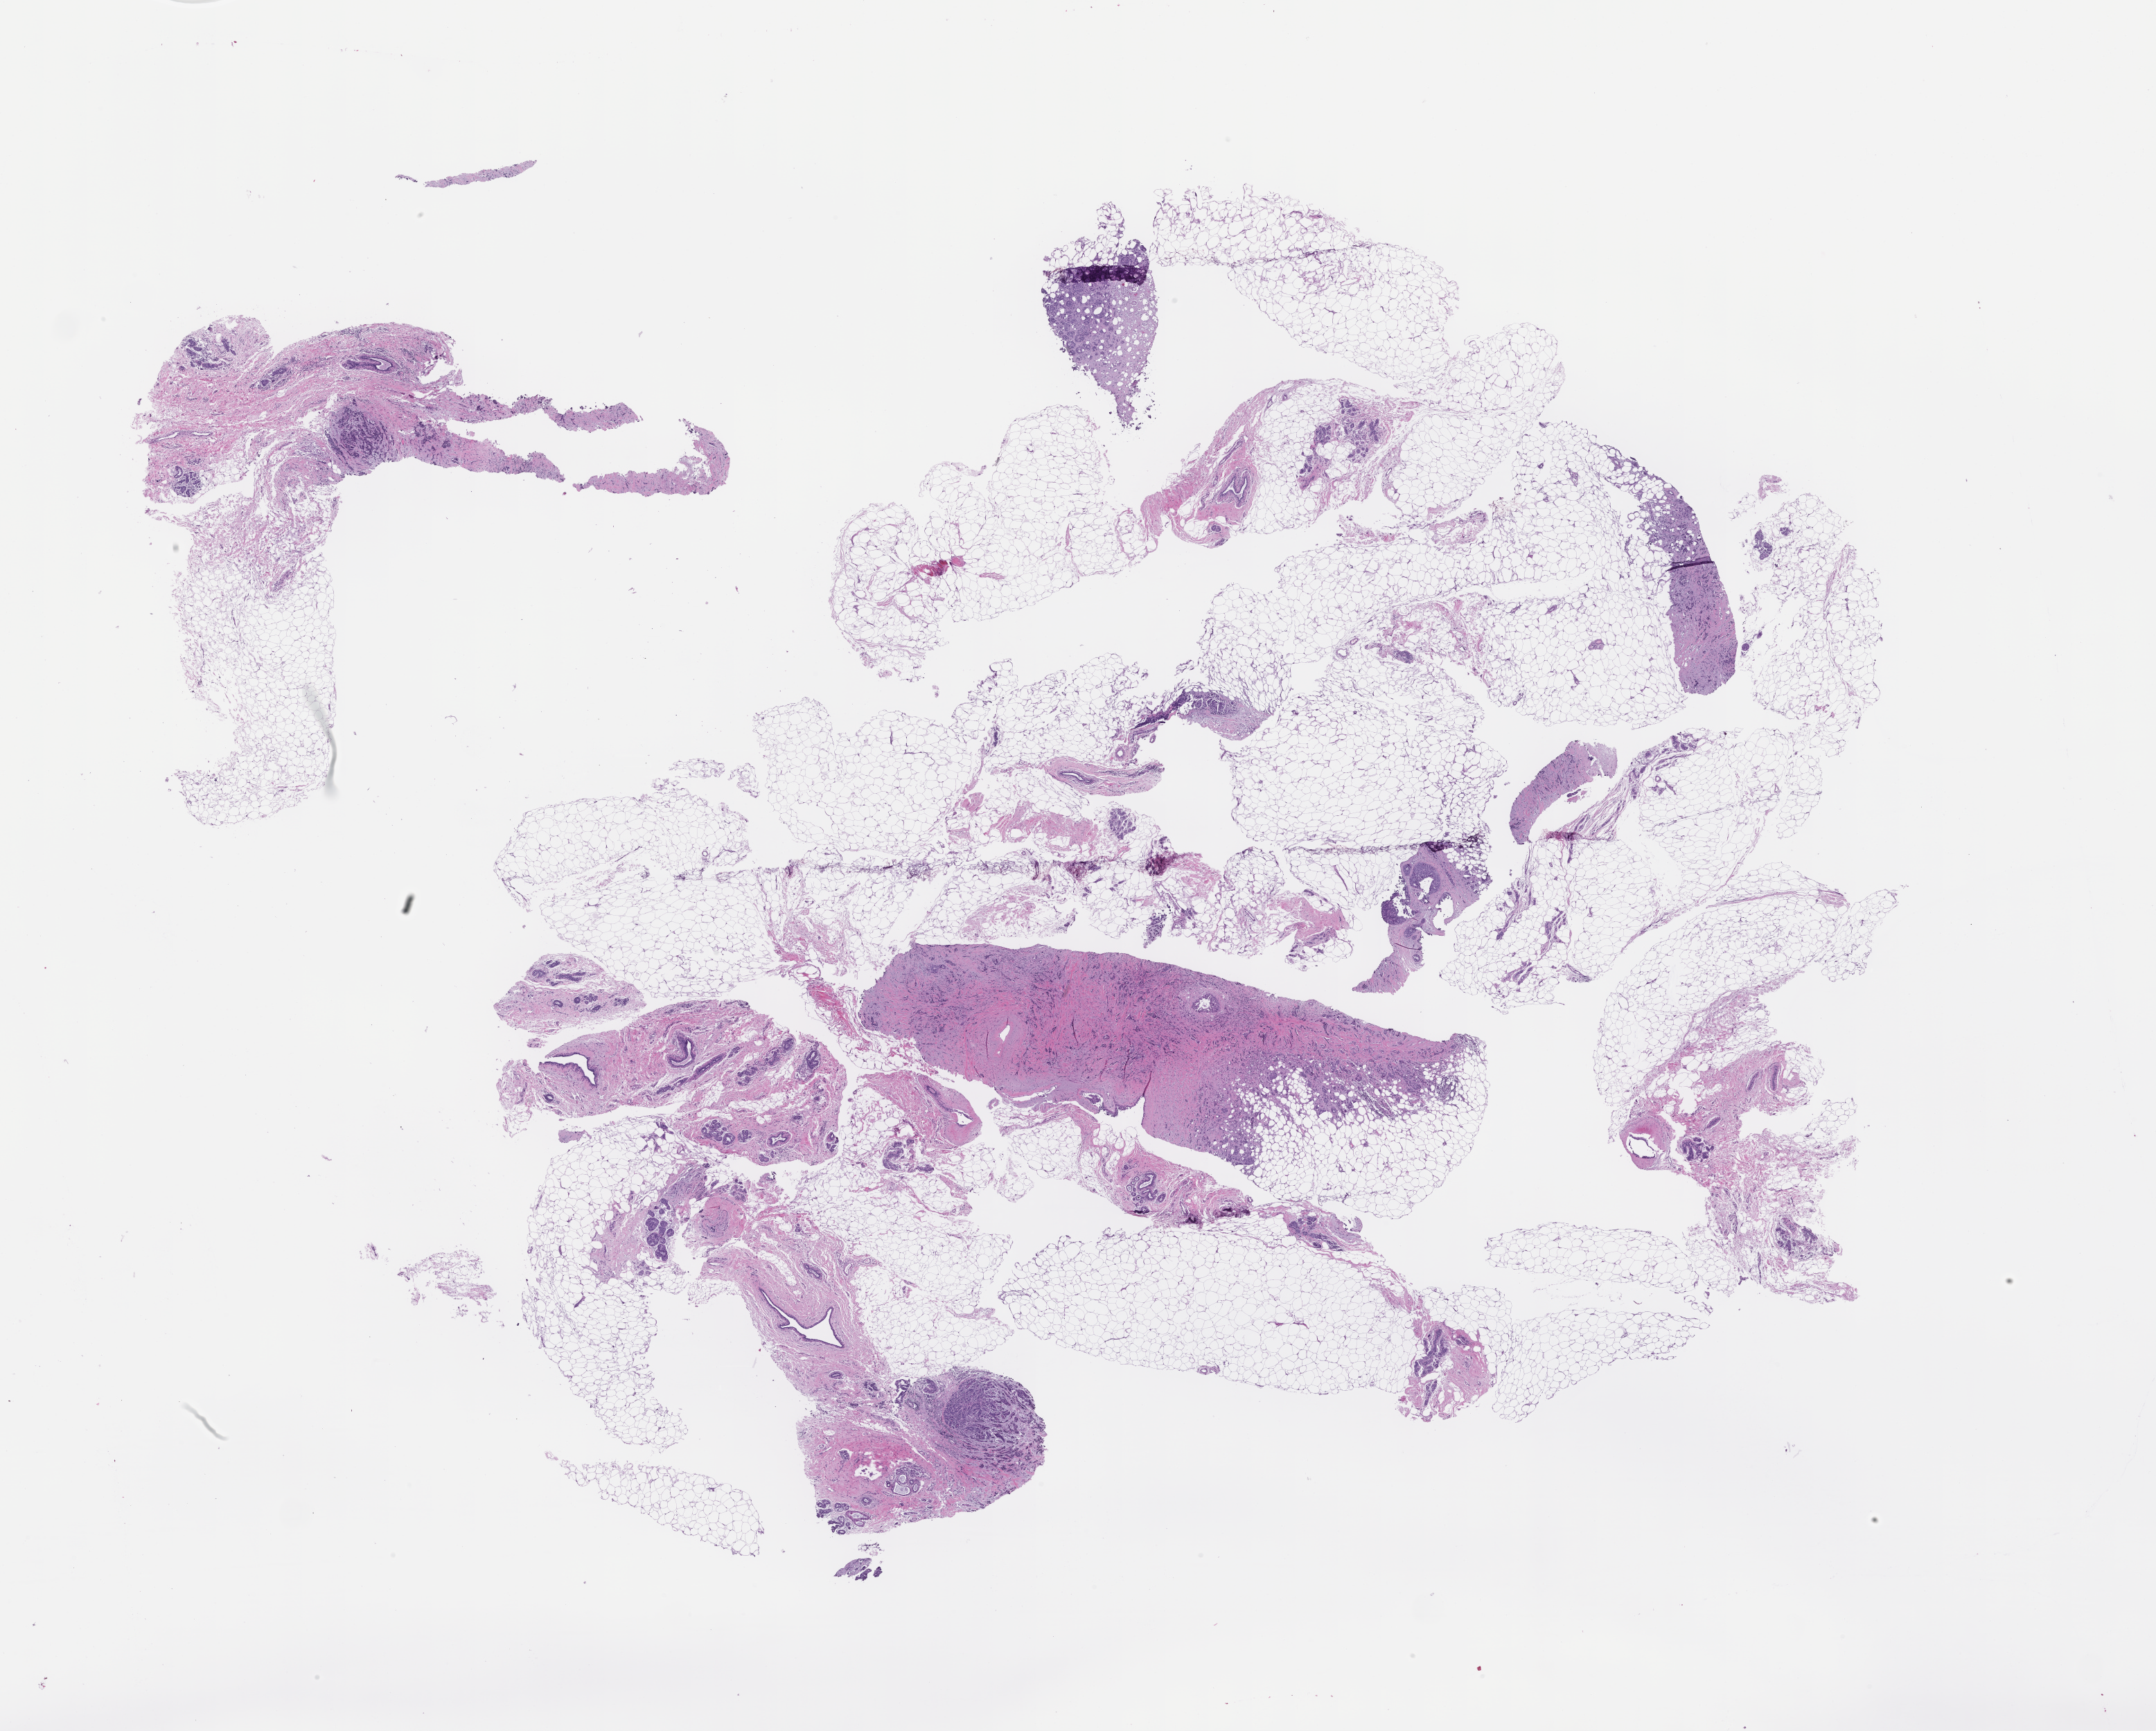
Whole-slide image, haematoxylin and eosin stain, low-resolution overview of the scanned area, about 25.1 x 20.2 mm; FFPE section; tissue site: breast. Female patient.
This section: primary tumour tissue. Diagnosis: Invasive Breast Carcinoma.